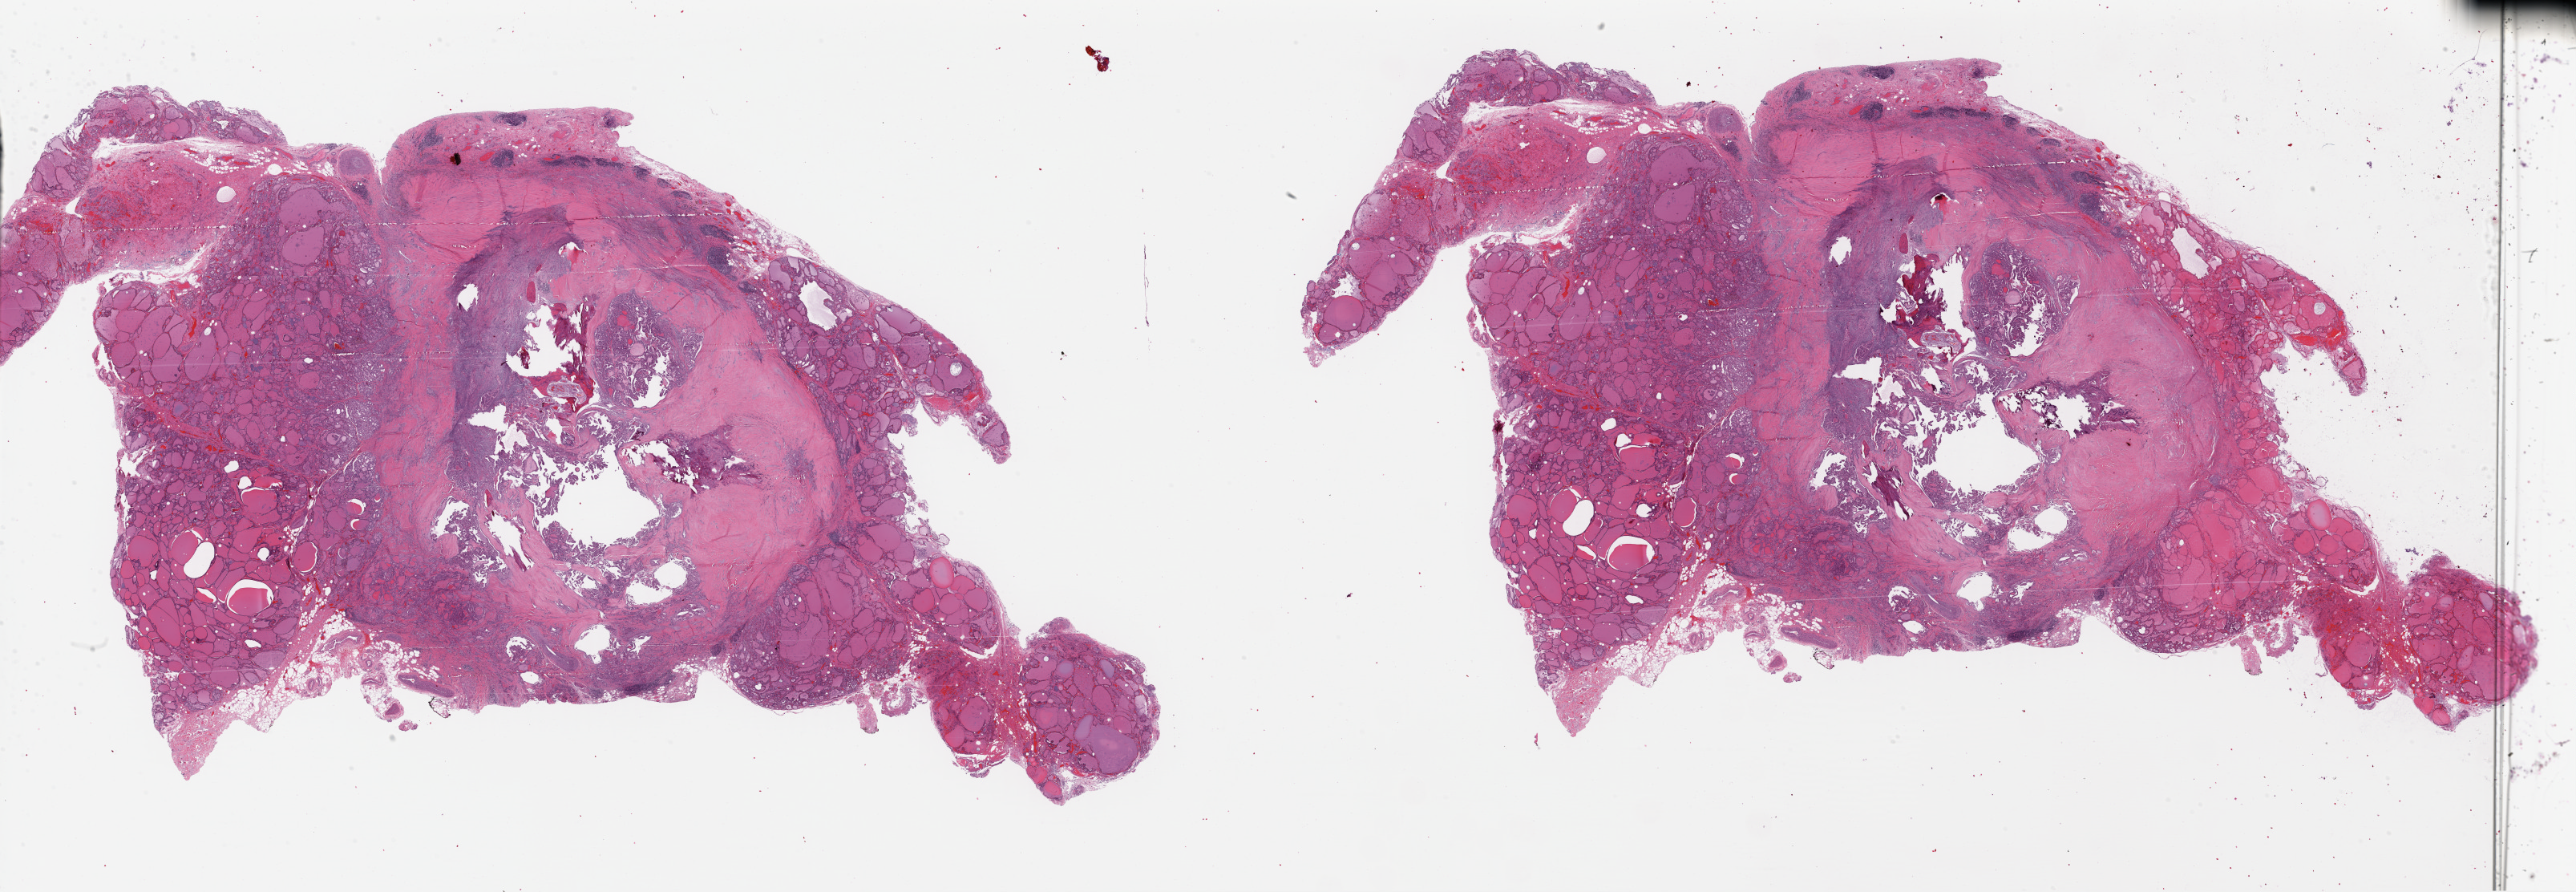
Digitized Hematoxylin and eosin (H&E) stained tissue section (whole slide) — a low-resolution overview of the entire scanned area, about 50.5 x 17.5 mm (from a 40x scan). Formalin-fixed paraffin-embedded (FFPE) diagnostic section. Sample: primary tumour, thyroid. Patient: male, age at initial diagnosis 63 years.
* lymph nodes positive (case pathology): 0 of 1 examined
* AJCC pathologic stage: III (7th edition)
* pathologic diagnosis: Papillary adenocarcinoma, NOS (thyroid gland)